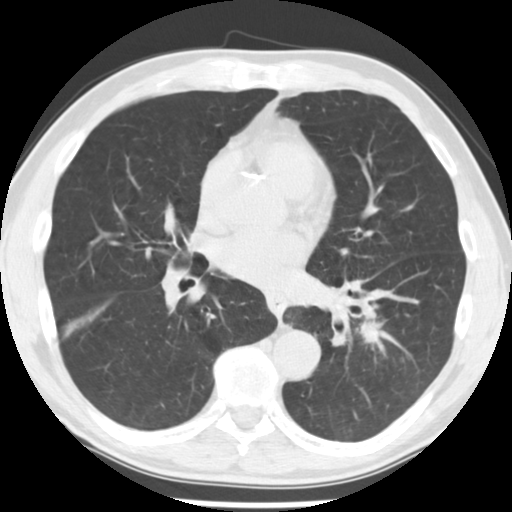
Axial slice from a low-dose chest CT screening exam; third screening round (two years after baseline); lung window (W 1500 / L -600 HU); 2.5 mm slice thickness; standard (soft-tissue) reconstruction kernel (STANDARD); slice 113 of 242 in the series; 512 × 512 image matrix, field of view 321 × 321 mm. Male participant, aged 64 years at enrolment.
• Expert-annotated lung lesion, bounding box [x1, y1, x2, y2] px = [352, 318, 390, 348].
• Screening reader's record for this exam: no non-calcified nodule ≥4 mm recorded.